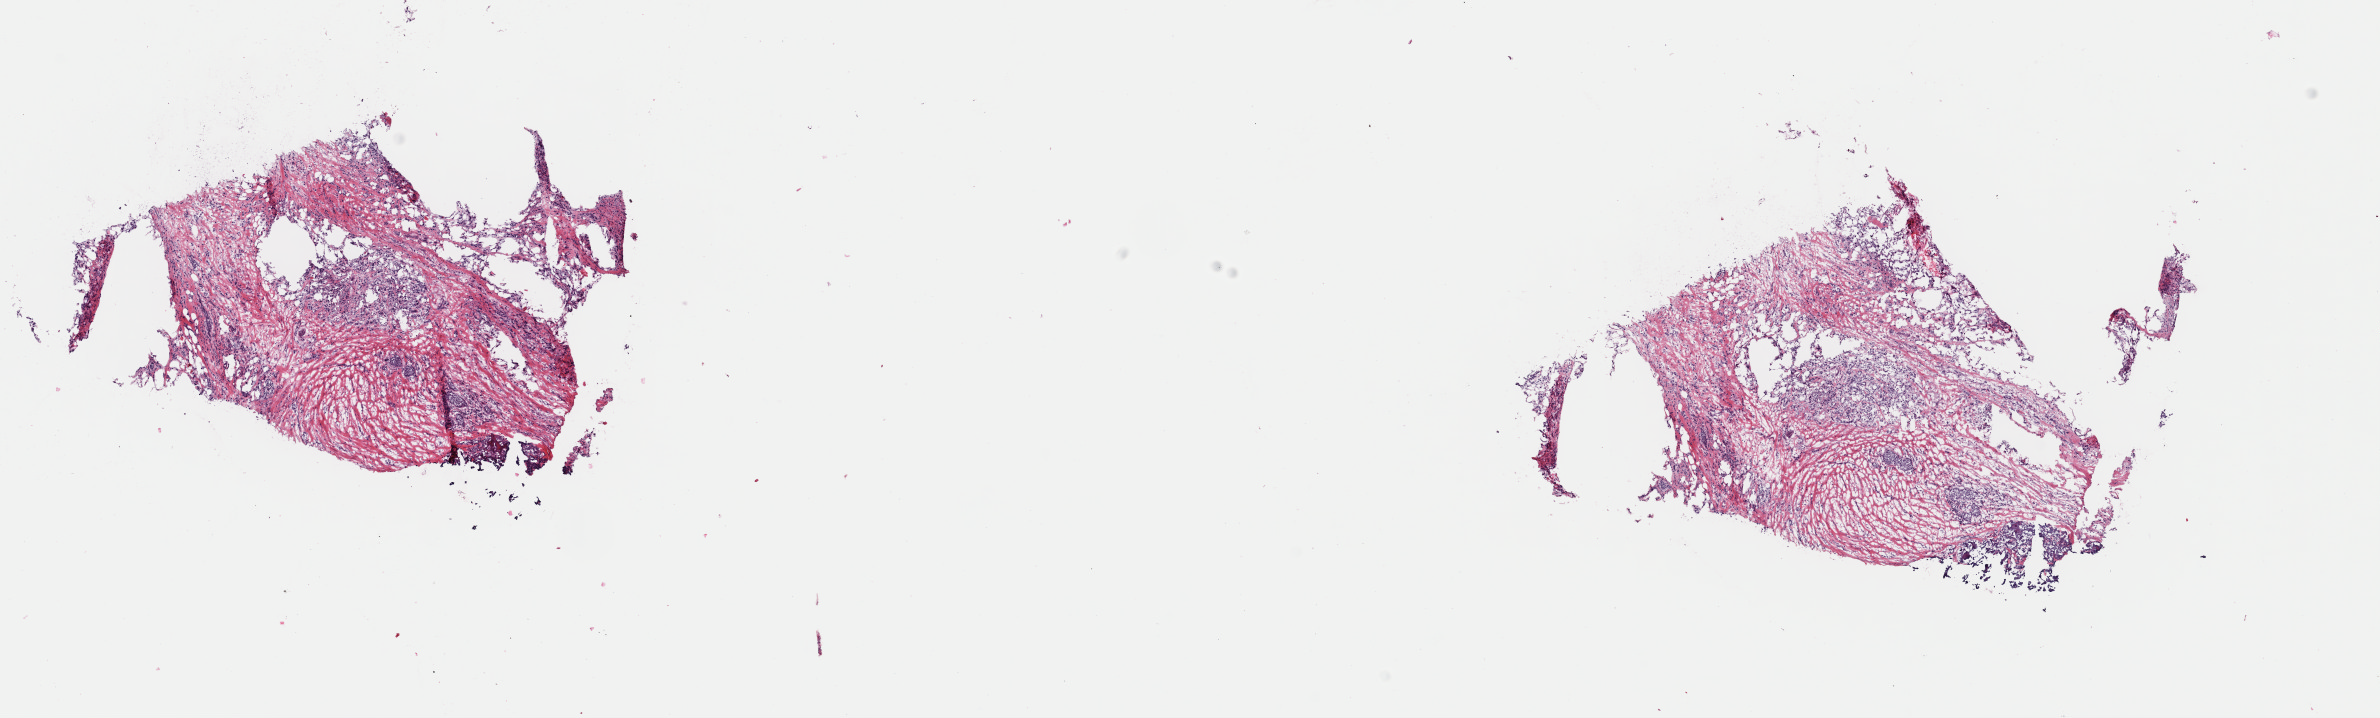
H&E whole-slide image — low-resolution overview of the scanned area, about 18.8 x 5.7 mm, frozen section, primary tumour sample from the breast. Female patient; age at initial diagnosis 56 years. Slide review estimates, as recorded: tumour cells 33%, tumour nuclei 75%, normal cells 1%, stromal cells 65%, necrosis 1%. Inflammatory infiltration, as recorded: lymphocyte infiltration 1%, monocyte infiltration 0%, neutrophil infiltration 0%.
* AJCC pathologic stage: I
* TNM: T1 N0 (i+) M0
* lymph nodes positive (case pathology): 0 of 1 examined
* histologic diagnosis: Lobular carcinoma, NOS